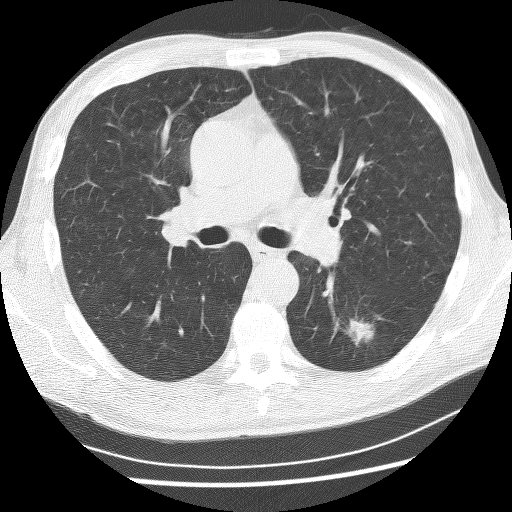
Axial slice from a low-dose chest CT screening exam, baseline screening round, lung window (W 1500 / L -600 HU), 2.5 mm slice thickness, lung (sharp) reconstruction kernel (BONE), slice 103 of 253 in the series. Male participant, aged 62 years at enrolment. Current smoker at enrolment.
• Expert reader's lesion annotation, box from (x=332, y=309) to (x=381, y=355) px.
• The exam's reader record, not a measurement of the box and not confirmed to be the same lesion: non-calcified nodule or mass ≥4 mm, left lower lobe, 21 × 17 mm, spiculated (stellate) margins, soft tissue attenuation.
• Official screen result: positive, change unspecified: nodule(s) >= 4 mm or enlarging nodule(s), mass(es), or other non-specific abnormalities suspicious for lung cancer.
• Lung cancer was diagnosed 58 days after this screen: non-small cell carcinoma, left lower lobe, poorly differentiated (G3), stage IA (AJCC 6th edition), 11 mm at pathology.